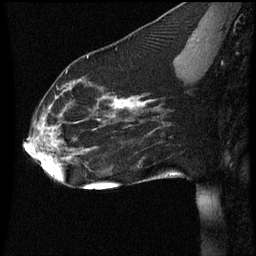
Breast MRI (dynamic contrast-enhanced), one sagittal slice. Slice 23 of 60 in the series (ordered by position). Dynamic contrast-enhanced series, image 2 of 3 at this slice position (ordered by acquisition). 1.5 T. TE 4.2 ms, TR 8.9 ms. 2 mm slice thickness. 256 × 256 image matrix, field of view 200 × 200 mm. Patient: female, 35 years. From the clinical record (not read from this slice): setting: breast cancer imaged before/during neoadjuvant chemotherapy; receptor status: HER2-positive.
Annotated regions visible in this slice (semi-automatically segmented with operator editing):
- analysis volume of interest (the breast-tissue region the enhancement analysis was run in; not a lesion): bounding box [x1, y1, x2, y2] px = [22, 66, 177, 177]
- tumour enhancement mask (voxels above the 70 % enhancement threshold inside the analysis volume of interest): [37, 86, 151, 155]